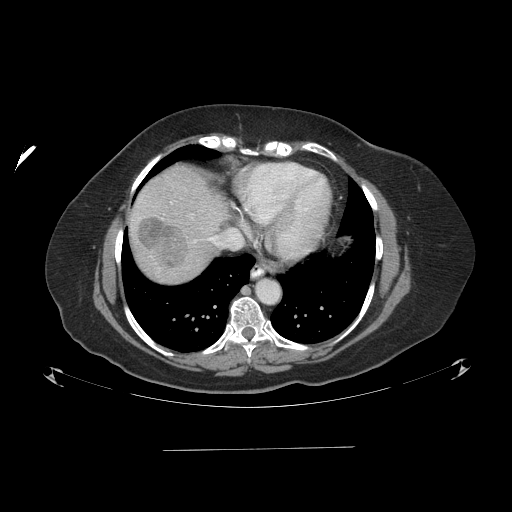
Contrast-enhanced abdominal CT (liver protocol), one axial slice. Position 80 of 103 along the scan axis. 120 kVp. One of 2 acquisitions stored at this slice position. Soft-tissue window (W 400 / L 40 HU). 2.5 mm slice thickness. 512 × 512 image matrix. From the clinical record (not read from this slice): diagnosis: hepatocellular carcinoma (patient treated with transarterial chemoembolisation; whether this scan precedes or follows treatment is not stated here); TNM stage (as recorded): Stage-IIIA; Child-Pugh class: A; tumour size: 5.2 cm.
Structures marked on this image (semi-automatically segmented with operator editing):
- liver parenchyma outside the tumour (the mass and vessels are separate outlines, so this box may not span the whole liver): bounding box <128,164,228,282> (left, top, right, bottom; pixels)
- mass: <136,216,188,268>
- liver vessels: <195,238,212,241>